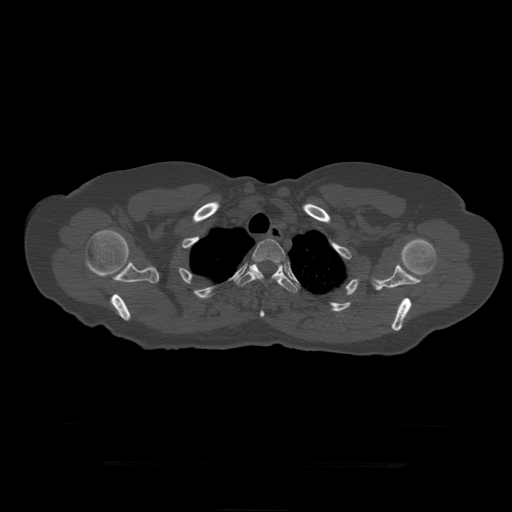
CT including the spine, one axial slice. Reconstruction kernel STANDARD. 120 kVp. Bone window (W 1800 / L 400 HU). 512 × 512 image matrix, field of view 450 × 450 mm. Patient age 41 years. Case-level facts recorded for this patient, not image findings: primary cancer: breast.
Annotated regions visible in this slice (semi-automatic segmentation, software-assisted and operator-edited):
- T3 vertebra: bounding box (x1, y1, x2, y2) in pixels: (249, 239, 286, 283)
- T4 vertebra: (237, 263, 298, 318)